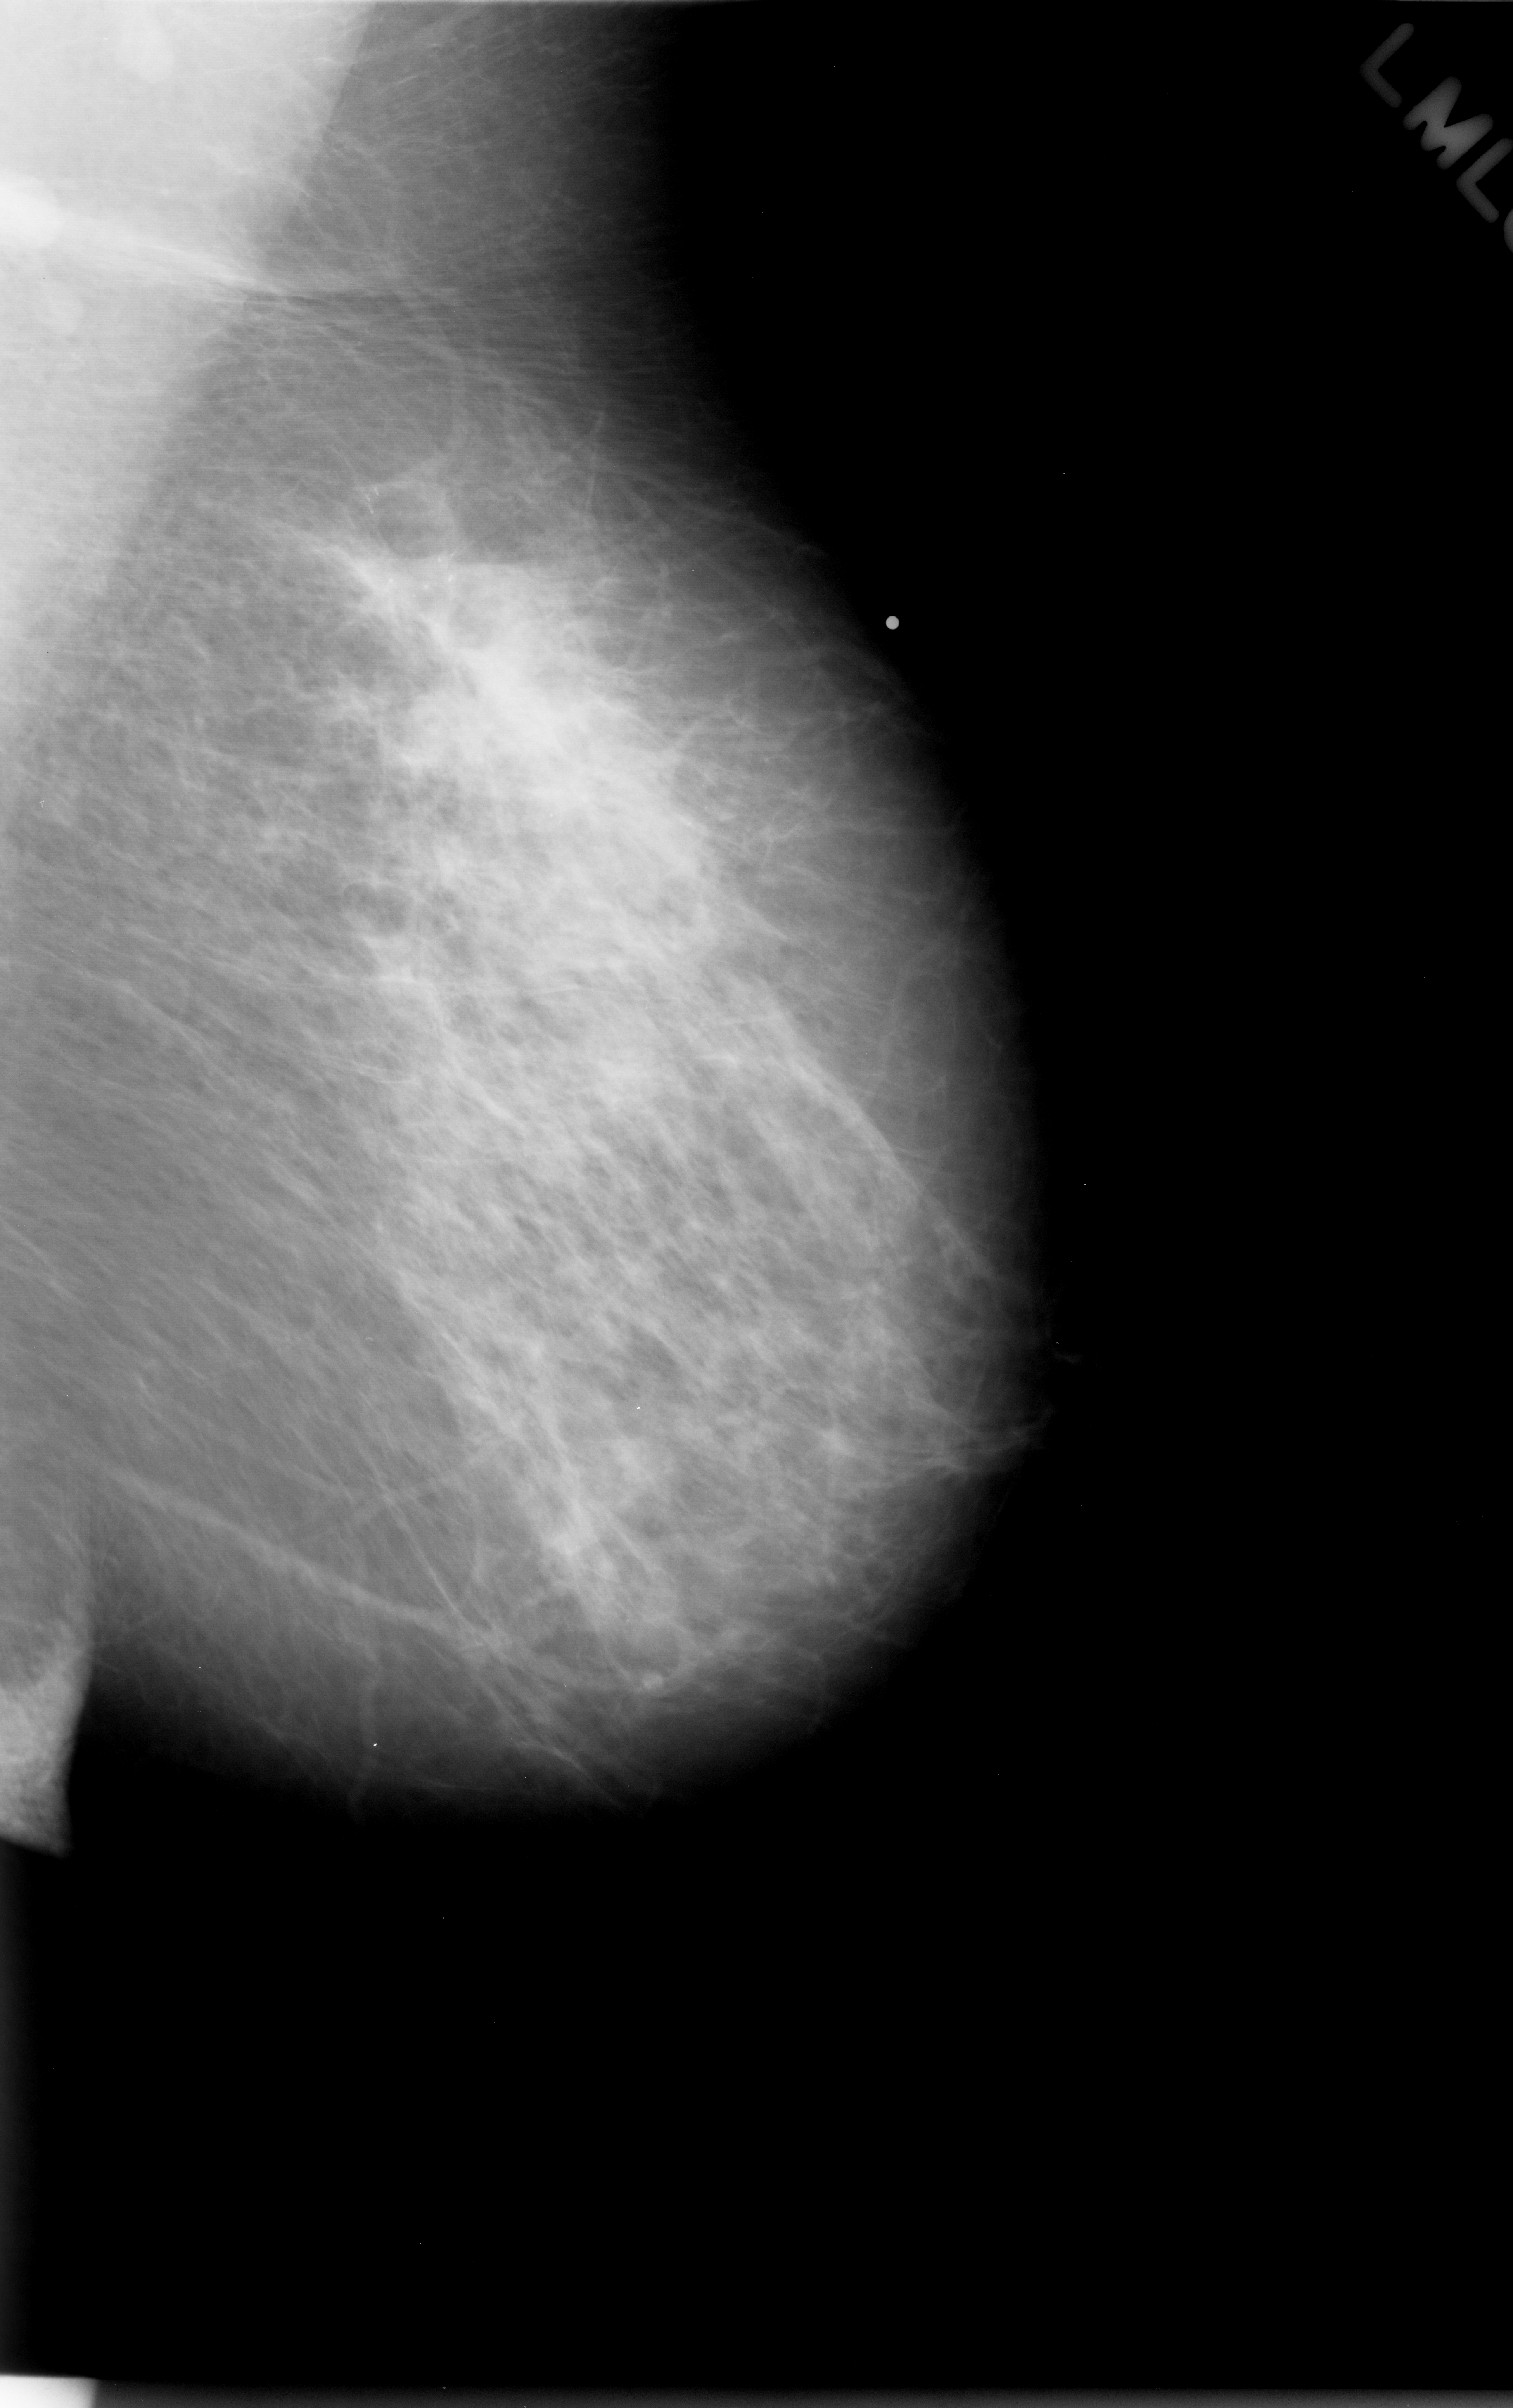
Scanned film-screen mammogram; left breast; mediolateral oblique (MLO) view; BI-RADS breast density category 2 (scale 1–4); 1513 × 2408 image matrix.
Expert-marked regions of interest on this image (one box per marked abnormality):
- calcifications, morphology pleomorphic, distribution regional; BI-RADS assessment category 4; subtlety rating 2 on a 1 (subtle) to 5 (obvious) scale; pathology (as recorded): malignant: bounding box (x1, y1, x2, y2) in pixels: (224, 436, 840, 1250)